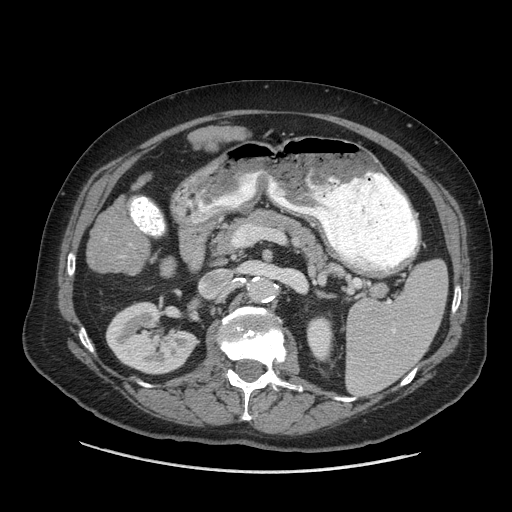
Contrast-enhanced abdominal CT (liver protocol), one axial slice. Slice 24 of 77 in the series (ordered by position). Reconstruction kernel STANDARD. 140 kVp. Soft-tissue window (W 400 / L 40 HU). 2.5 mm slice thickness. 512 × 512 image matrix, field of view 420 × 420 mm. From the clinical record (not read from this slice): diagnosis: hepatocellular carcinoma (patient treated with transarterial chemoembolisation; whether this scan precedes or follows treatment is not stated here); TNM stage (as recorded): Stage-I; Child-Pugh class: A; tumour differentiation: well differentiated; tumour nodularity: uninodular.
Annotated regions visible in this slice (semi-automatic segmentation, software-assisted and operator-edited):
- liver parenchyma outside the tumour (the mass and vessels are separate outlines, so this box may not span the whole liver): bounding box [x1, y1, x2, y2] px = [86, 196, 150, 274]